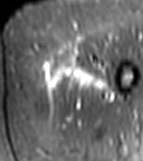
MRI of an extremity soft-tissue mass, one axial slice. Slice 13 of 81 in the series (ordered by position). STIR. MR volume resampled by the dataset authors to the PET/CT grid (not the native acquisition matrix). 143 × 161 image matrix. Female patient. From the clinical record (not read from this slice): histological type: myxofibrosarcoma; grade: intermediate; site of the primary tumour: left thigh.
Structures marked on this image (expert contour drawn on MRI and transferred to this co-registered scan by the dataset authors):
- gross tumour volume including surrounding oedema: bounding box [x1, y1, x2, y2] px = [38, 58, 112, 100]
- gross tumour volume (mass): [79, 60, 93, 66]